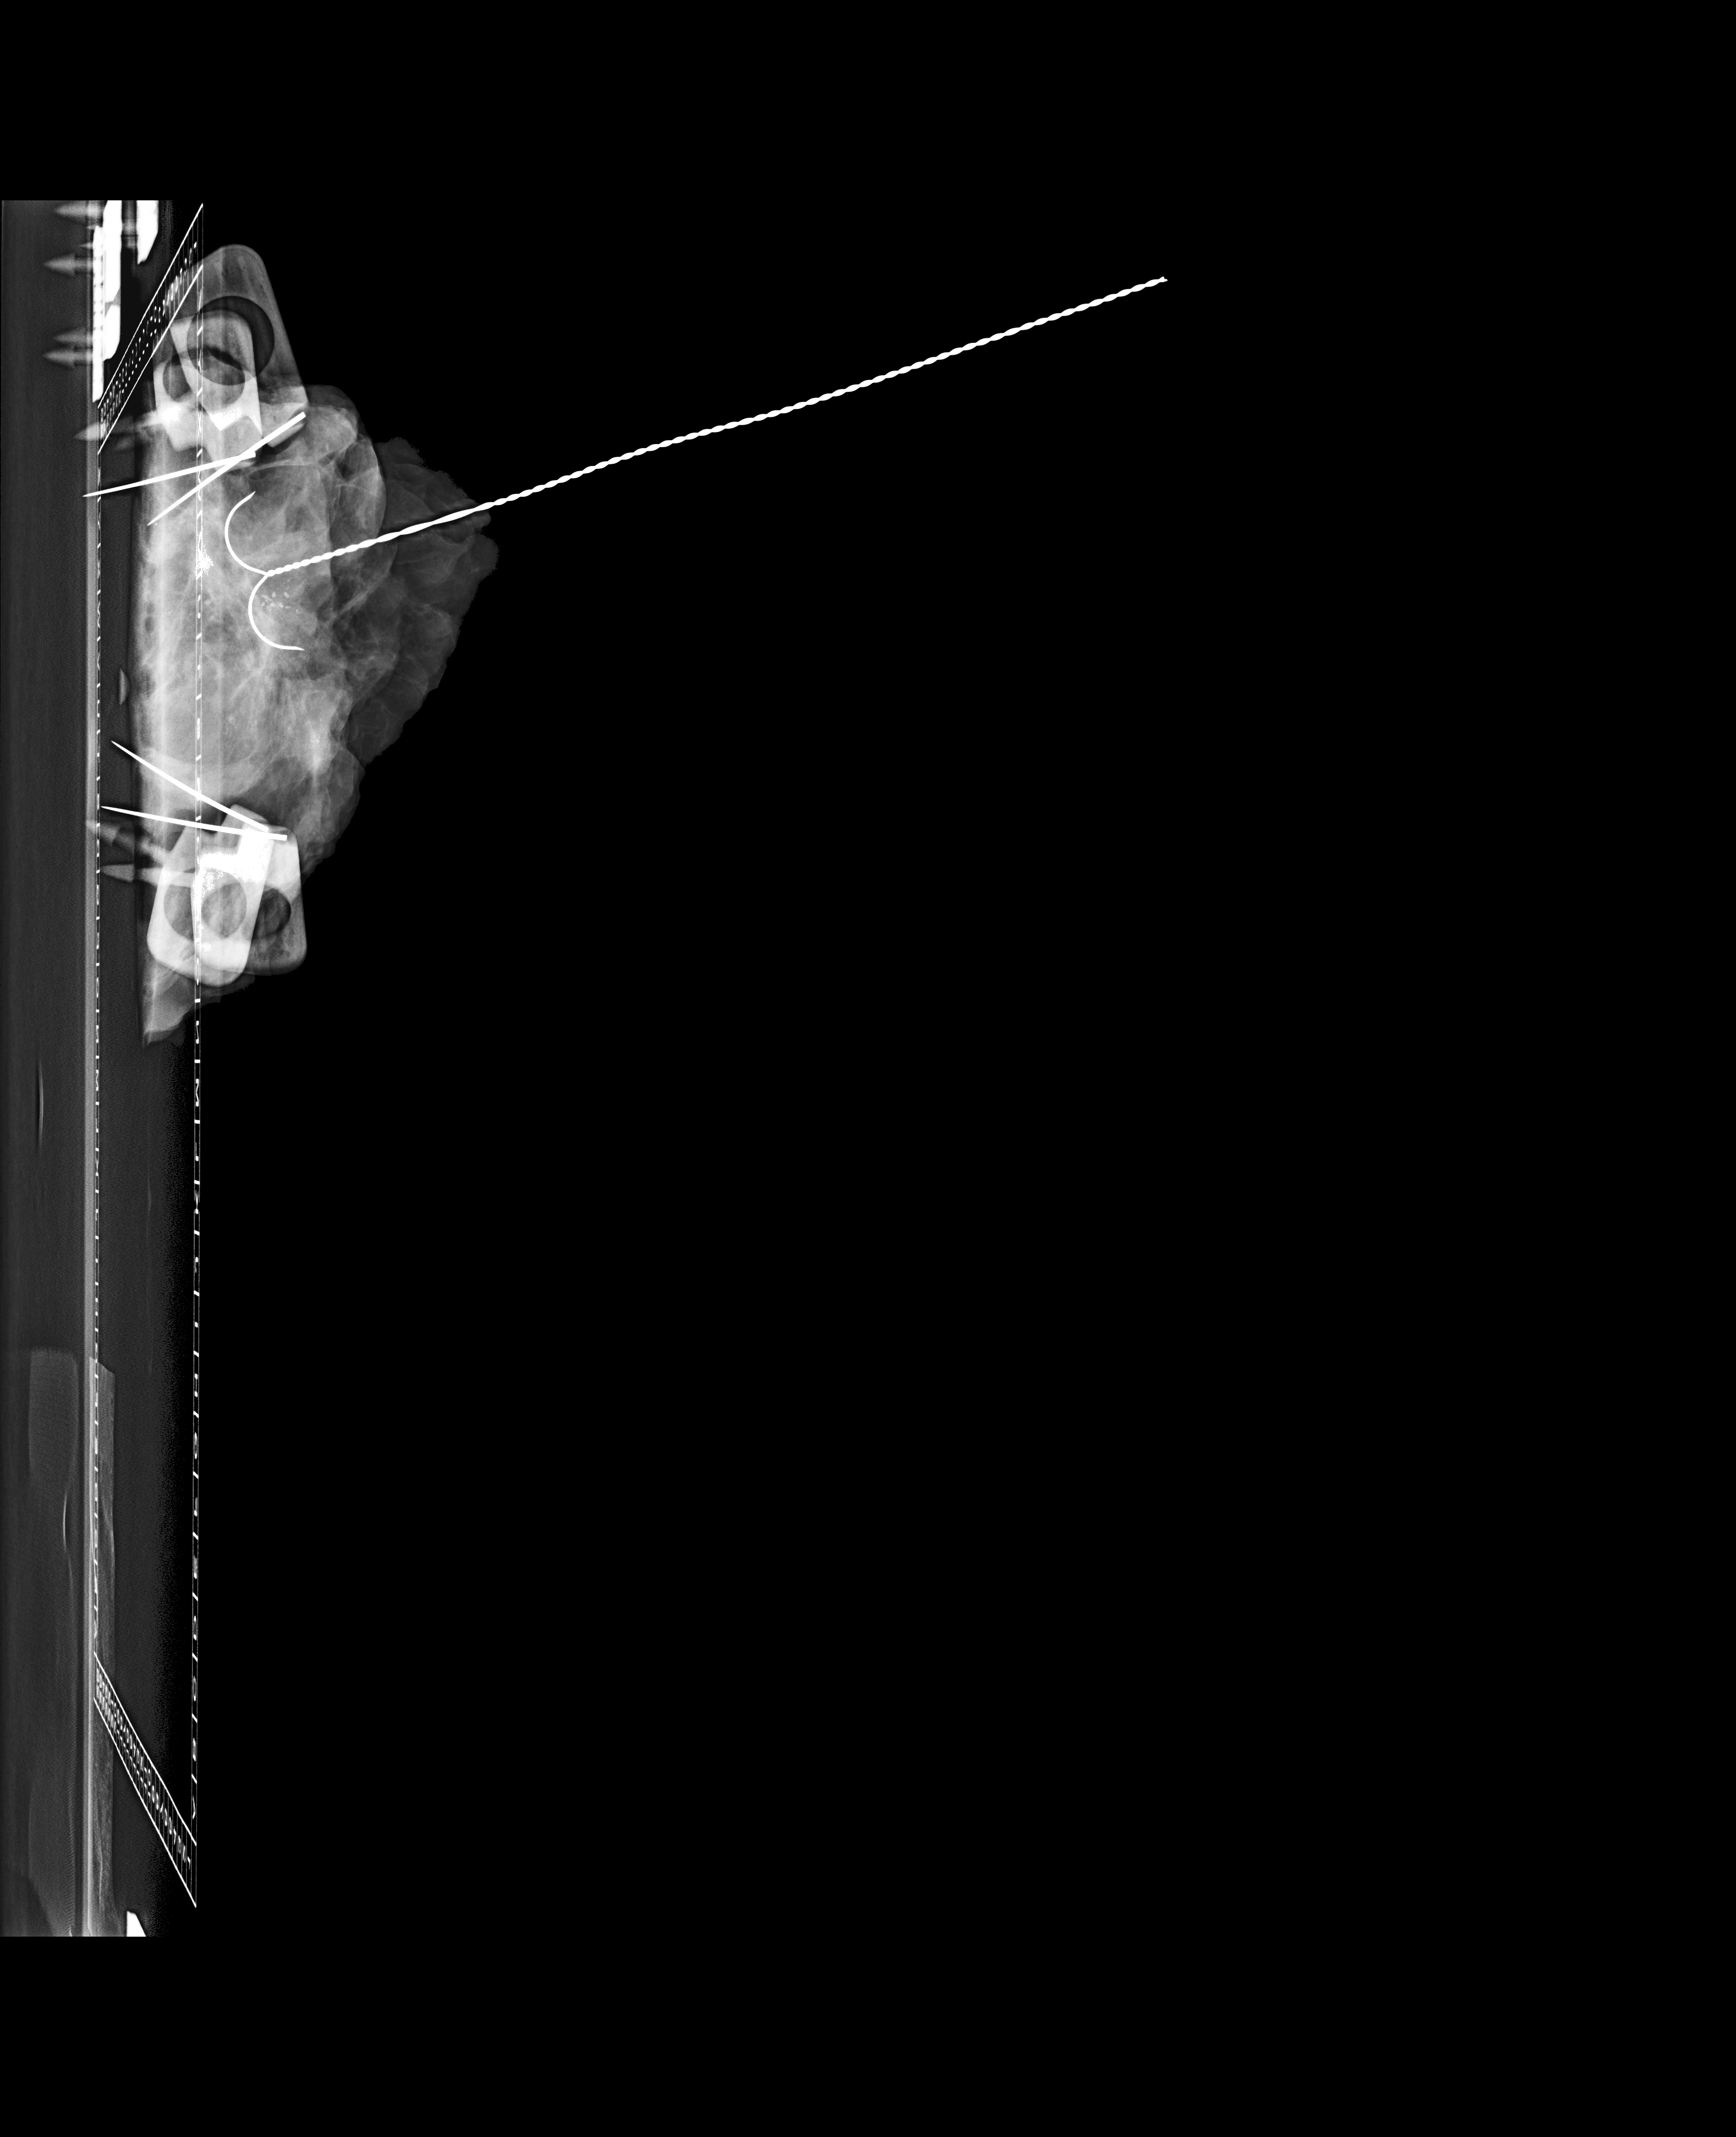
Diagnostic work-up study, compressed breast thickness 93 mm. Patient aged 79 years (female).
Image type: full-field digital mammogram. Breast: left. Projection: ML view.